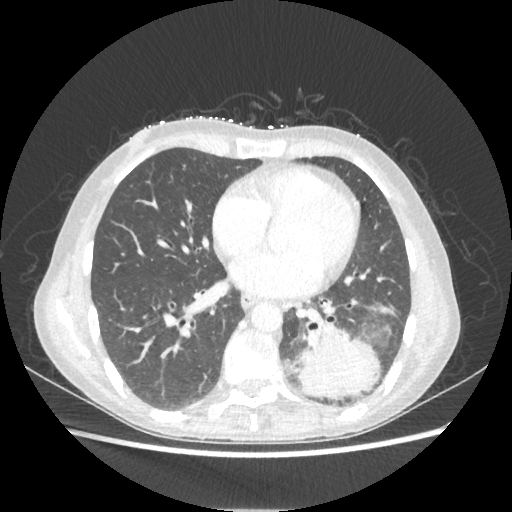
Chest CT, one axial slice. Position 94 of 221 along the scan axis. 80 kVp. Lung window (W 1500 / L -600 HU). 512 × 512 image matrix. Patient: female, 53 years. From the clinical record (not read from this slice): clinical TNM (as recorded): T3 N0 M0.
Annotated regions visible in this slice (bounding box drawn by a radiologist):
- lung tumour (recorded histology: adenocarcinoma): bounding box [x1, y1, x2, y2] px = [297, 325, 383, 400]